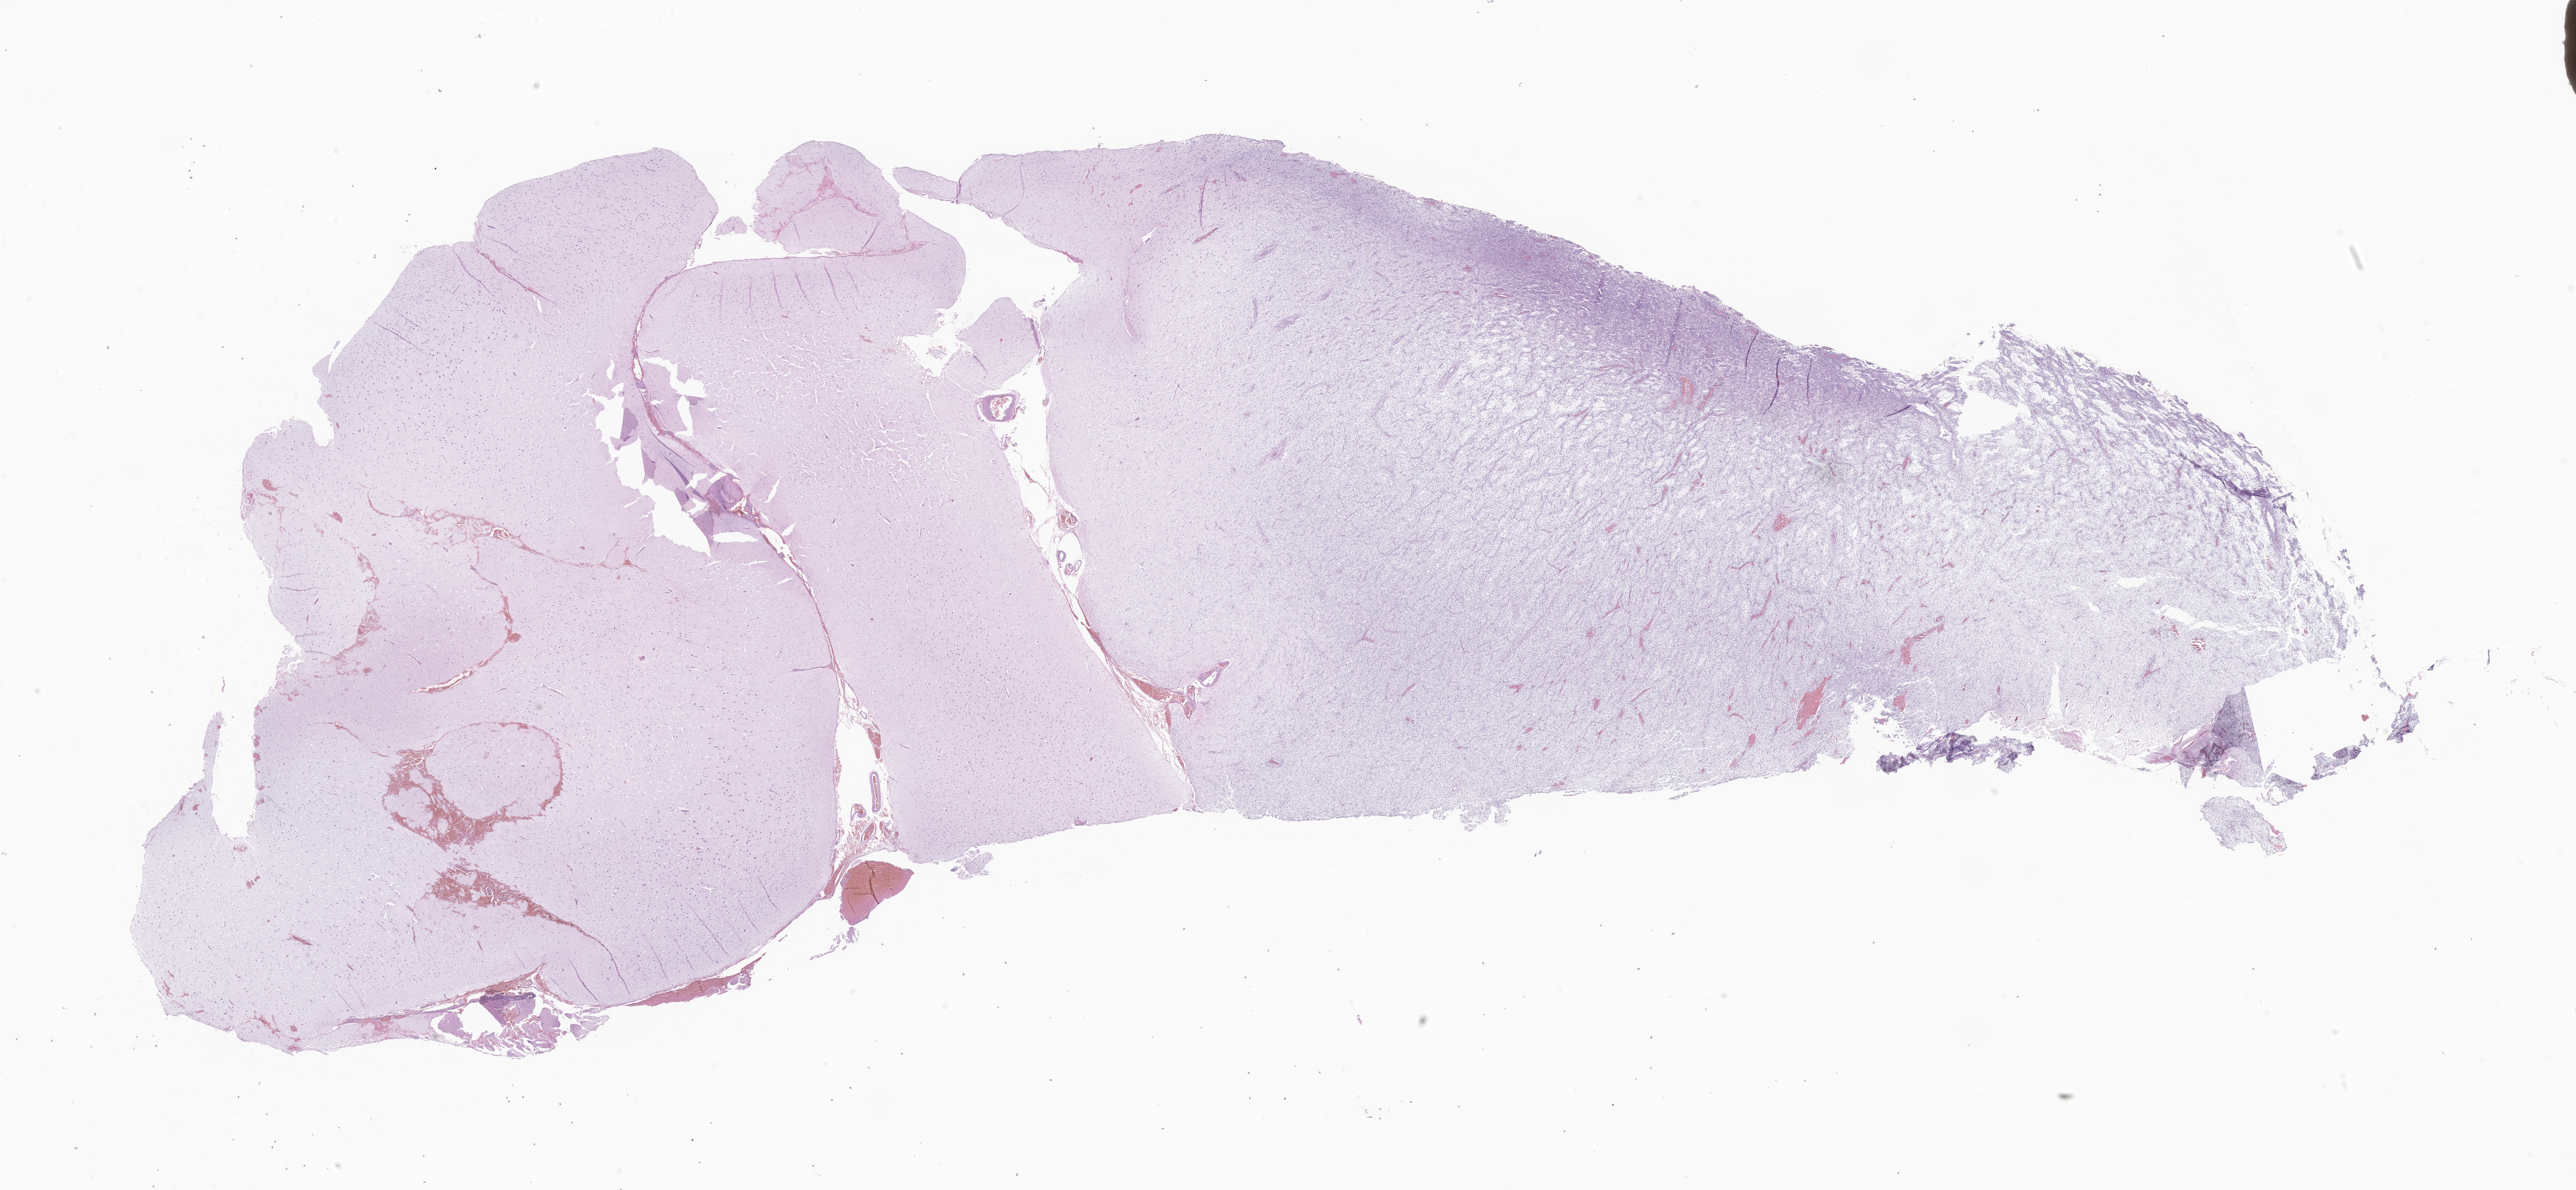
Whole-slide image, haematoxylin and eosin stain of tumor tissue from the brain, whole scanned area (about 36.8 x 17.0 mm) shown as a low-resolution overview, FFPE section. Patient female; age 53 months (4 years 5 months).
• recorded diagnosis: Neoplasm, uncertain whether benign or malignant